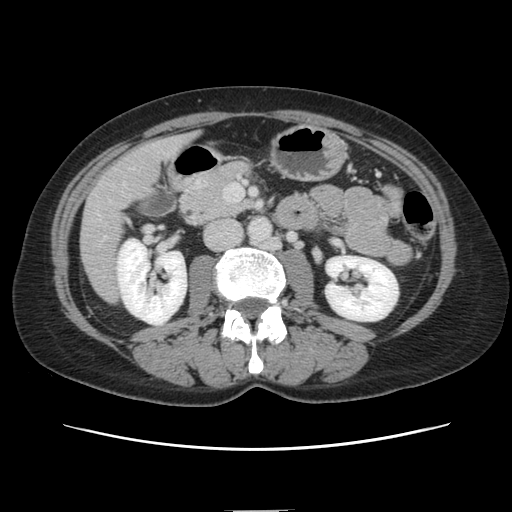
Contrast-enhanced abdominal CT, one axial slice; position 43 of 141 along the scan axis; soft-tissue window (W 400 / L 40 HU); 2.5 mm slice thickness; 512 × 512 image matrix, field of view 350 × 350 mm. Female patient, age 63 years. From the clinical record (not read from this slice): diagnosis: colorectal cancer liver metastases, imaged before liver resection; multiple liver metastases: yes; largest metastasis: 3.2 cm.
Structures marked on this image (manually delineated by an expert):
- liver: bounding box [x1, y1, x2, y2] px = [81, 135, 193, 302]
- planned liver remnant (the part of the liver to remain after resection): [184, 136, 193, 145]